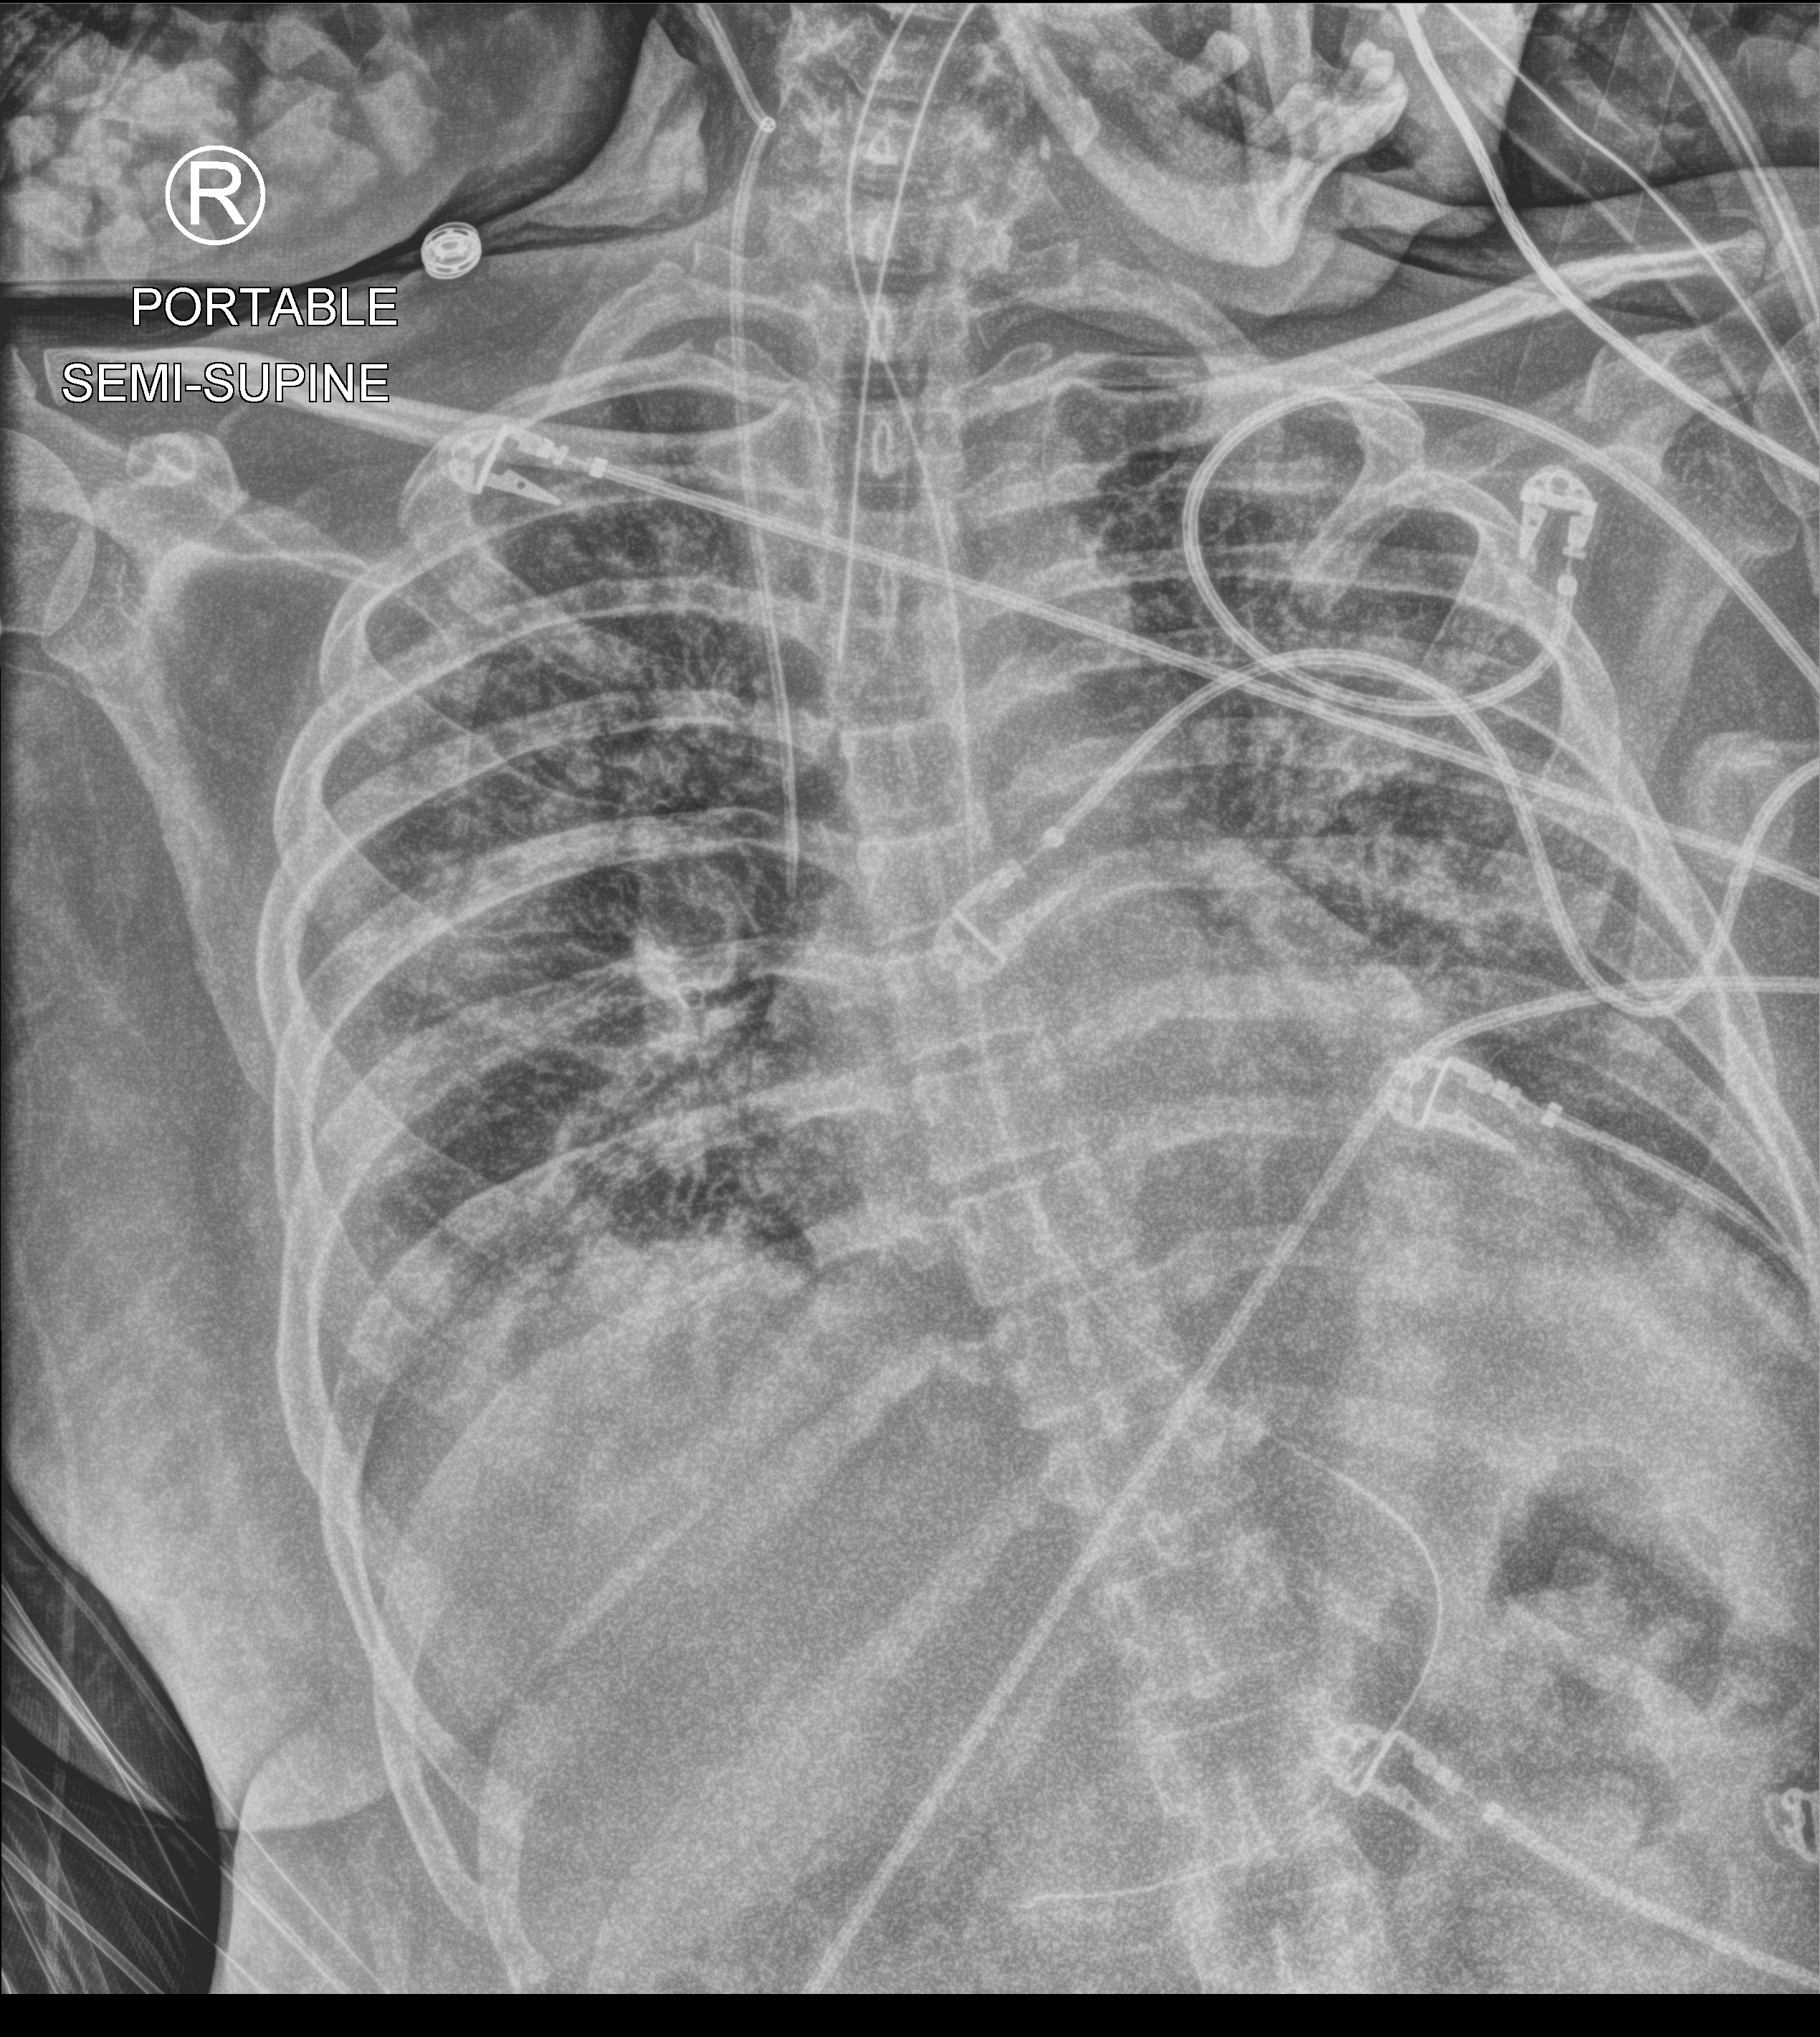
Bedside chest radiograph (computed radiography), anteroposterior (AP) projection. Adult patient hospitalised with COVID-19, age 18–59 years.
From the hospital-stay record, not from the radiograph (when in the stay this image was taken is not recorded): length of hospital stay: 15 days; admitted to intensive care during this hospital stay: yes.